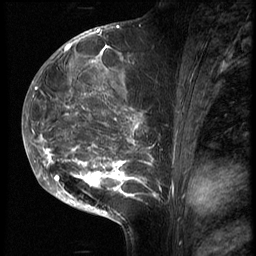
Breast MRI (dynamic contrast-enhanced), one sagittal slice. Position 32 of 70 along the scan axis. 3 images stored at this slice position (order not interpretable as contrast timing). 1.5 T. TE 4.2 ms, TR 9 ms. 2.5 mm slice thickness. 256 × 256 image matrix, field of view 180 × 180 mm. Female patient, age 28 years. Case-level facts recorded for this patient, not image findings: setting: breast cancer imaged before/during neoadjuvant chemotherapy.
Structures marked on this image (semi-automatically segmented with operator editing):
- analysis volume of interest (the breast-tissue region the enhancement analysis was run in; not a lesion): bounding box (x1, y1, x2, y2) in pixels: (43, 42, 171, 215)
- tumour enhancement mask (voxels above the 140 % enhancement threshold inside the analysis volume of interest): (43, 43, 160, 204)